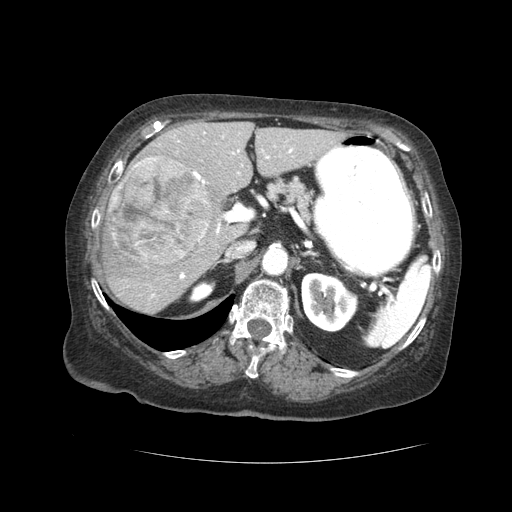
Contrast-enhanced abdominal CT (liver protocol), one axial slice. Position 22 of 59 along the scan axis. 120 kVp. Soft-tissue window (W 400 / L 40 HU). 2.5 mm slice thickness. 512 × 512 image matrix, field of view 380 × 380 mm. From the clinical record (not read from this slice): diagnosis: hepatocellular carcinoma (patient treated with transarterial chemoembolisation; whether this scan precedes or follows treatment is not stated here); TNM stage (as recorded): Stage-I; Child-Pugh class: A; tumour nodularity: uninodular.
Structures marked on this image (semi-automatically segmented with operator editing):
- liver parenchyma outside the tumour (the mass and vessels are separate outlines, so this box may not span the whole liver): bounding box [x1, y1, x2, y2] px = [102, 122, 342, 312]
- mass: [106, 158, 210, 266]
- liver vessels: [150, 132, 294, 298]